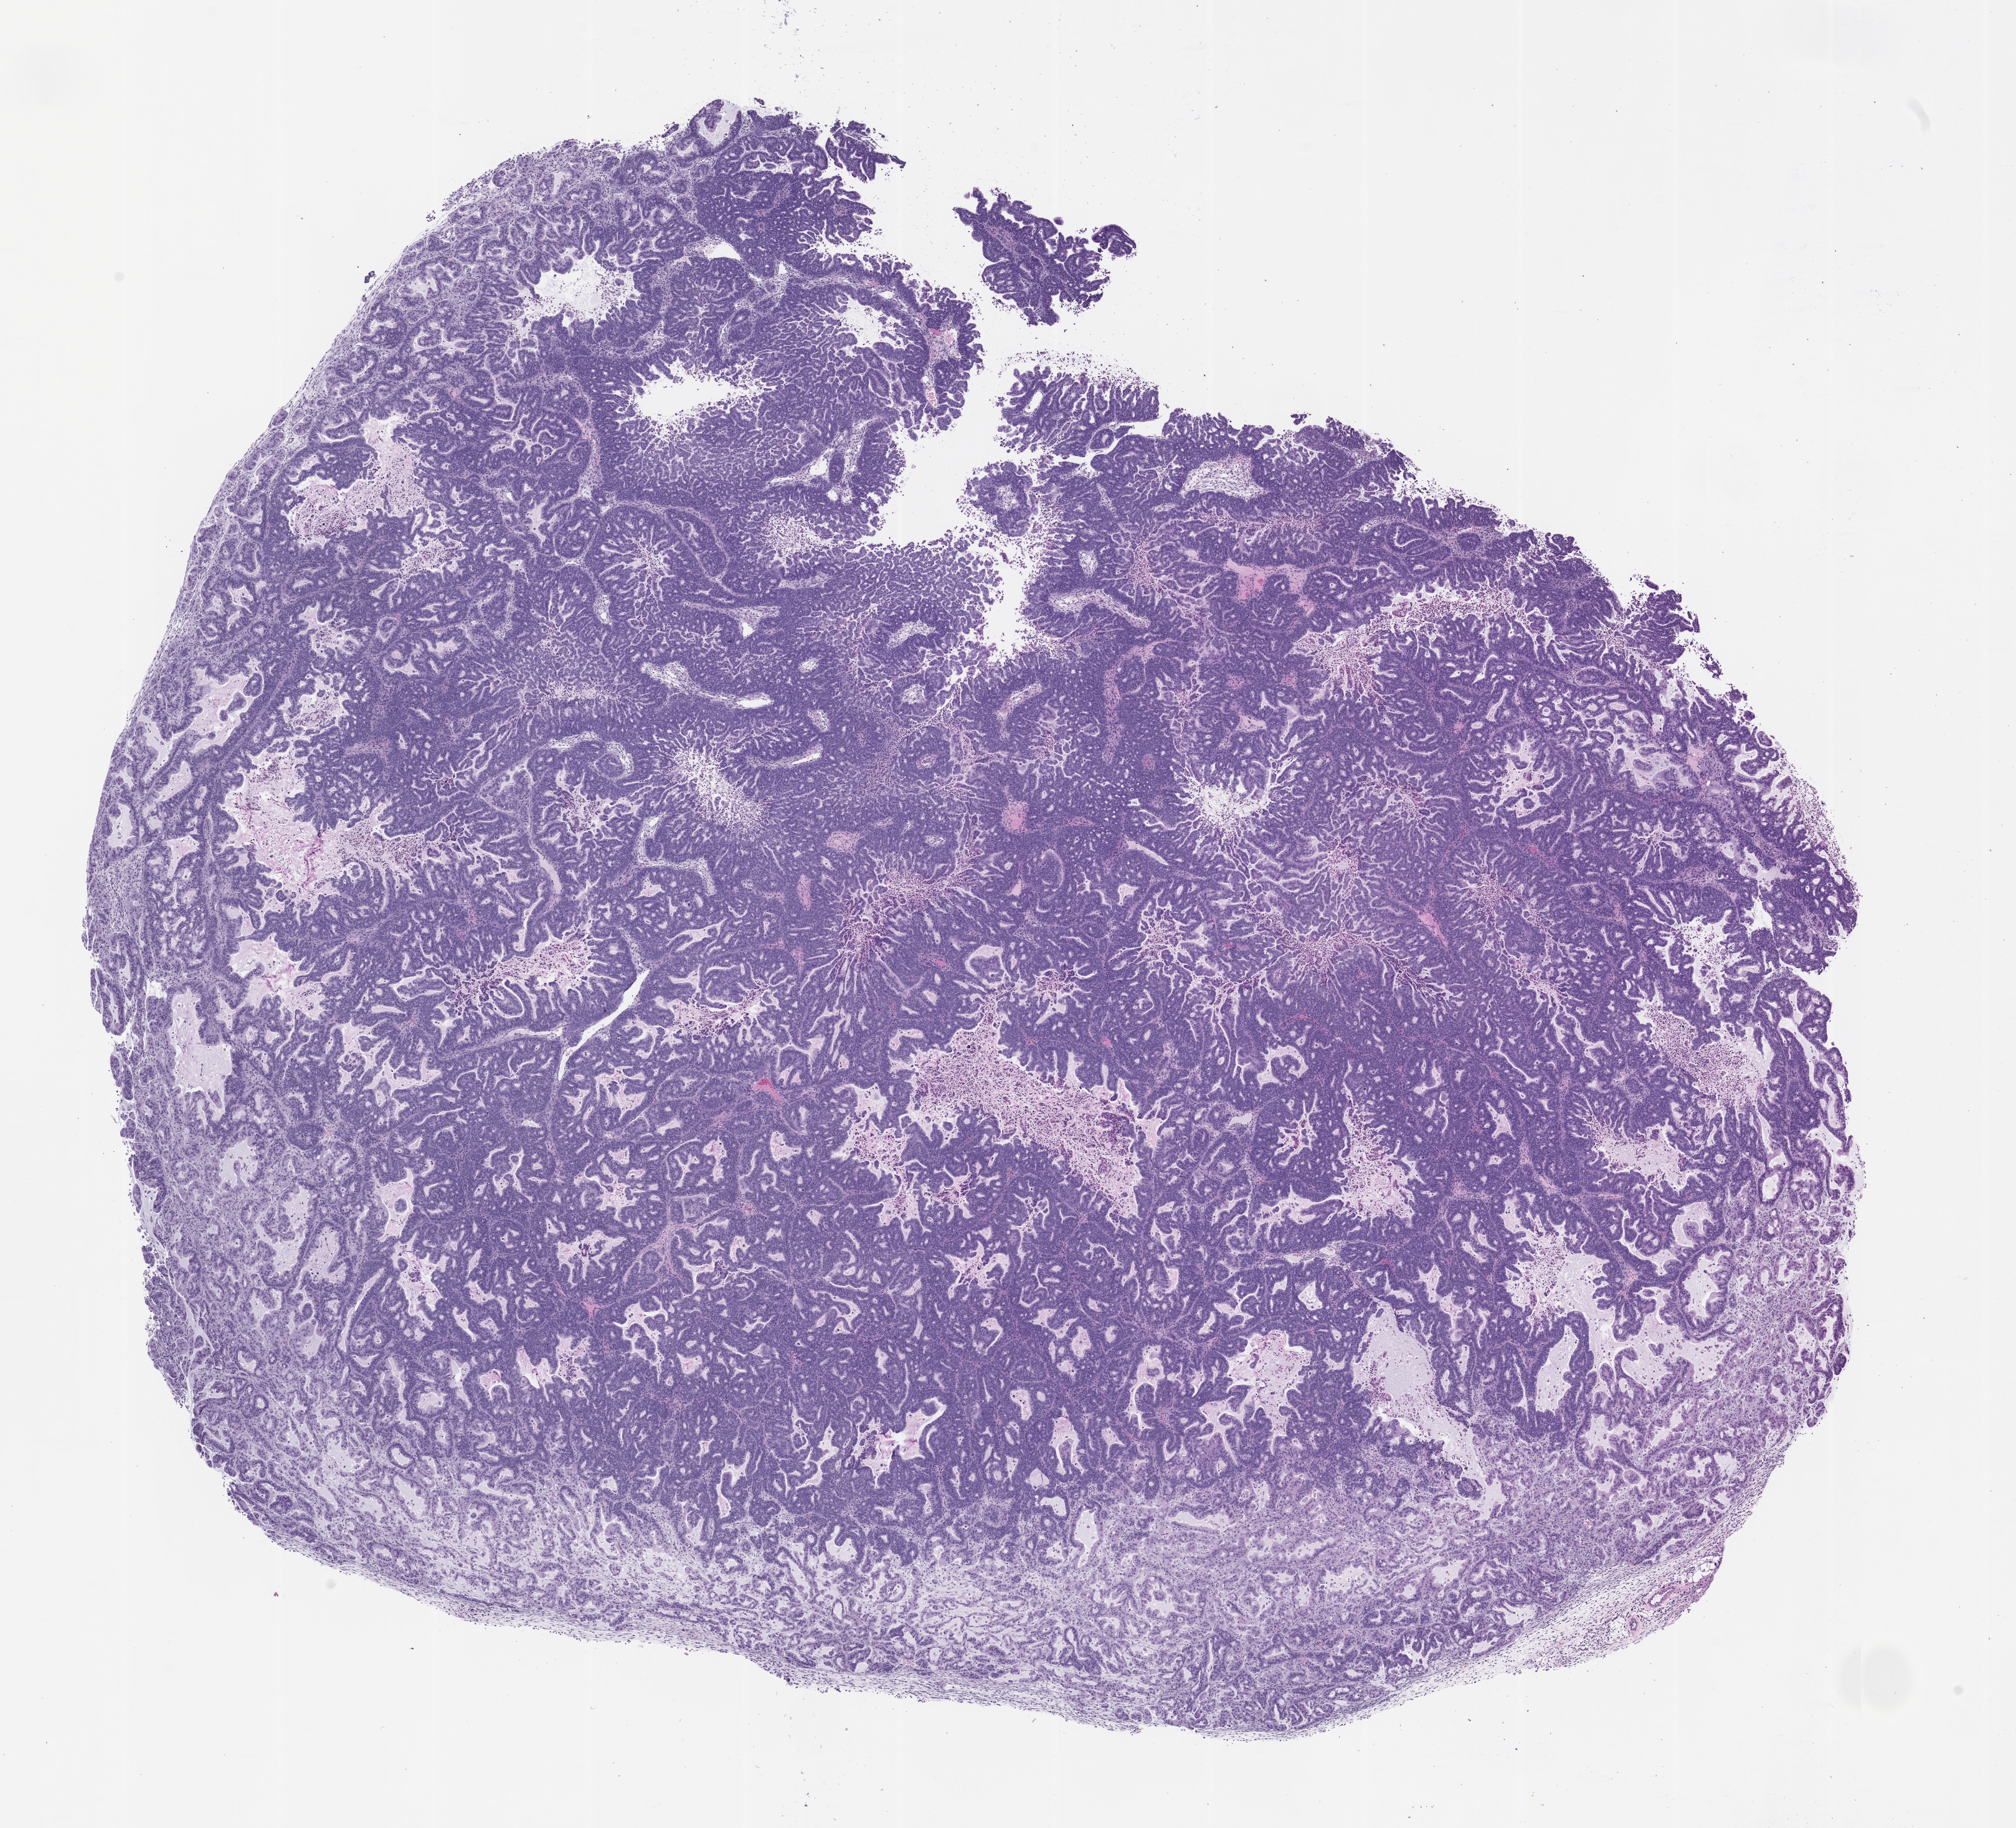
Whole-slide image, H&E: patient-derived xenograft (human tumor grown in a mouse), passage 2, shown as a low-resolution overview of the whole scanned area (about 13.0 x 11.8 mm). FFPE section. Originating tumor site category: pancreas.
* originating patient diagnosis: Pancreatic Adenocarcinoma